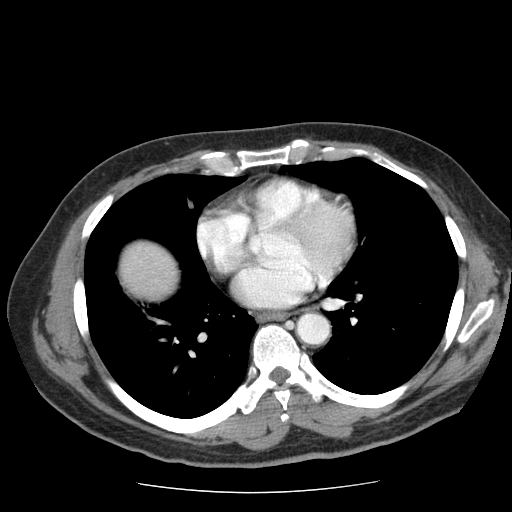
Contrast-enhanced abdominal CT (liver protocol), one axial slice; position 77 of 85 along the scan axis; 120 kVp; soft-tissue window (W 400 / L 40 HU); 512 × 512 image matrix, field of view 360 × 360 mm. From the clinical record (not read from this slice): diagnosis: hepatocellular carcinoma (patient treated with transarterial chemoembolisation; whether this scan precedes or follows treatment is not stated here); TNM stage (as recorded): Stage-IIIA; Child-Pugh class: A; tumour differentiation: well differentiated; tumour nodularity: multinodular.
Structures marked on this image (semi-automatically segmented with operator editing):
- liver parenchyma outside the tumour (the mass and vessels are separate outlines, so this box may not span the whole liver): bounding box <122,242,176,298> (left, top, right, bottom; pixels)